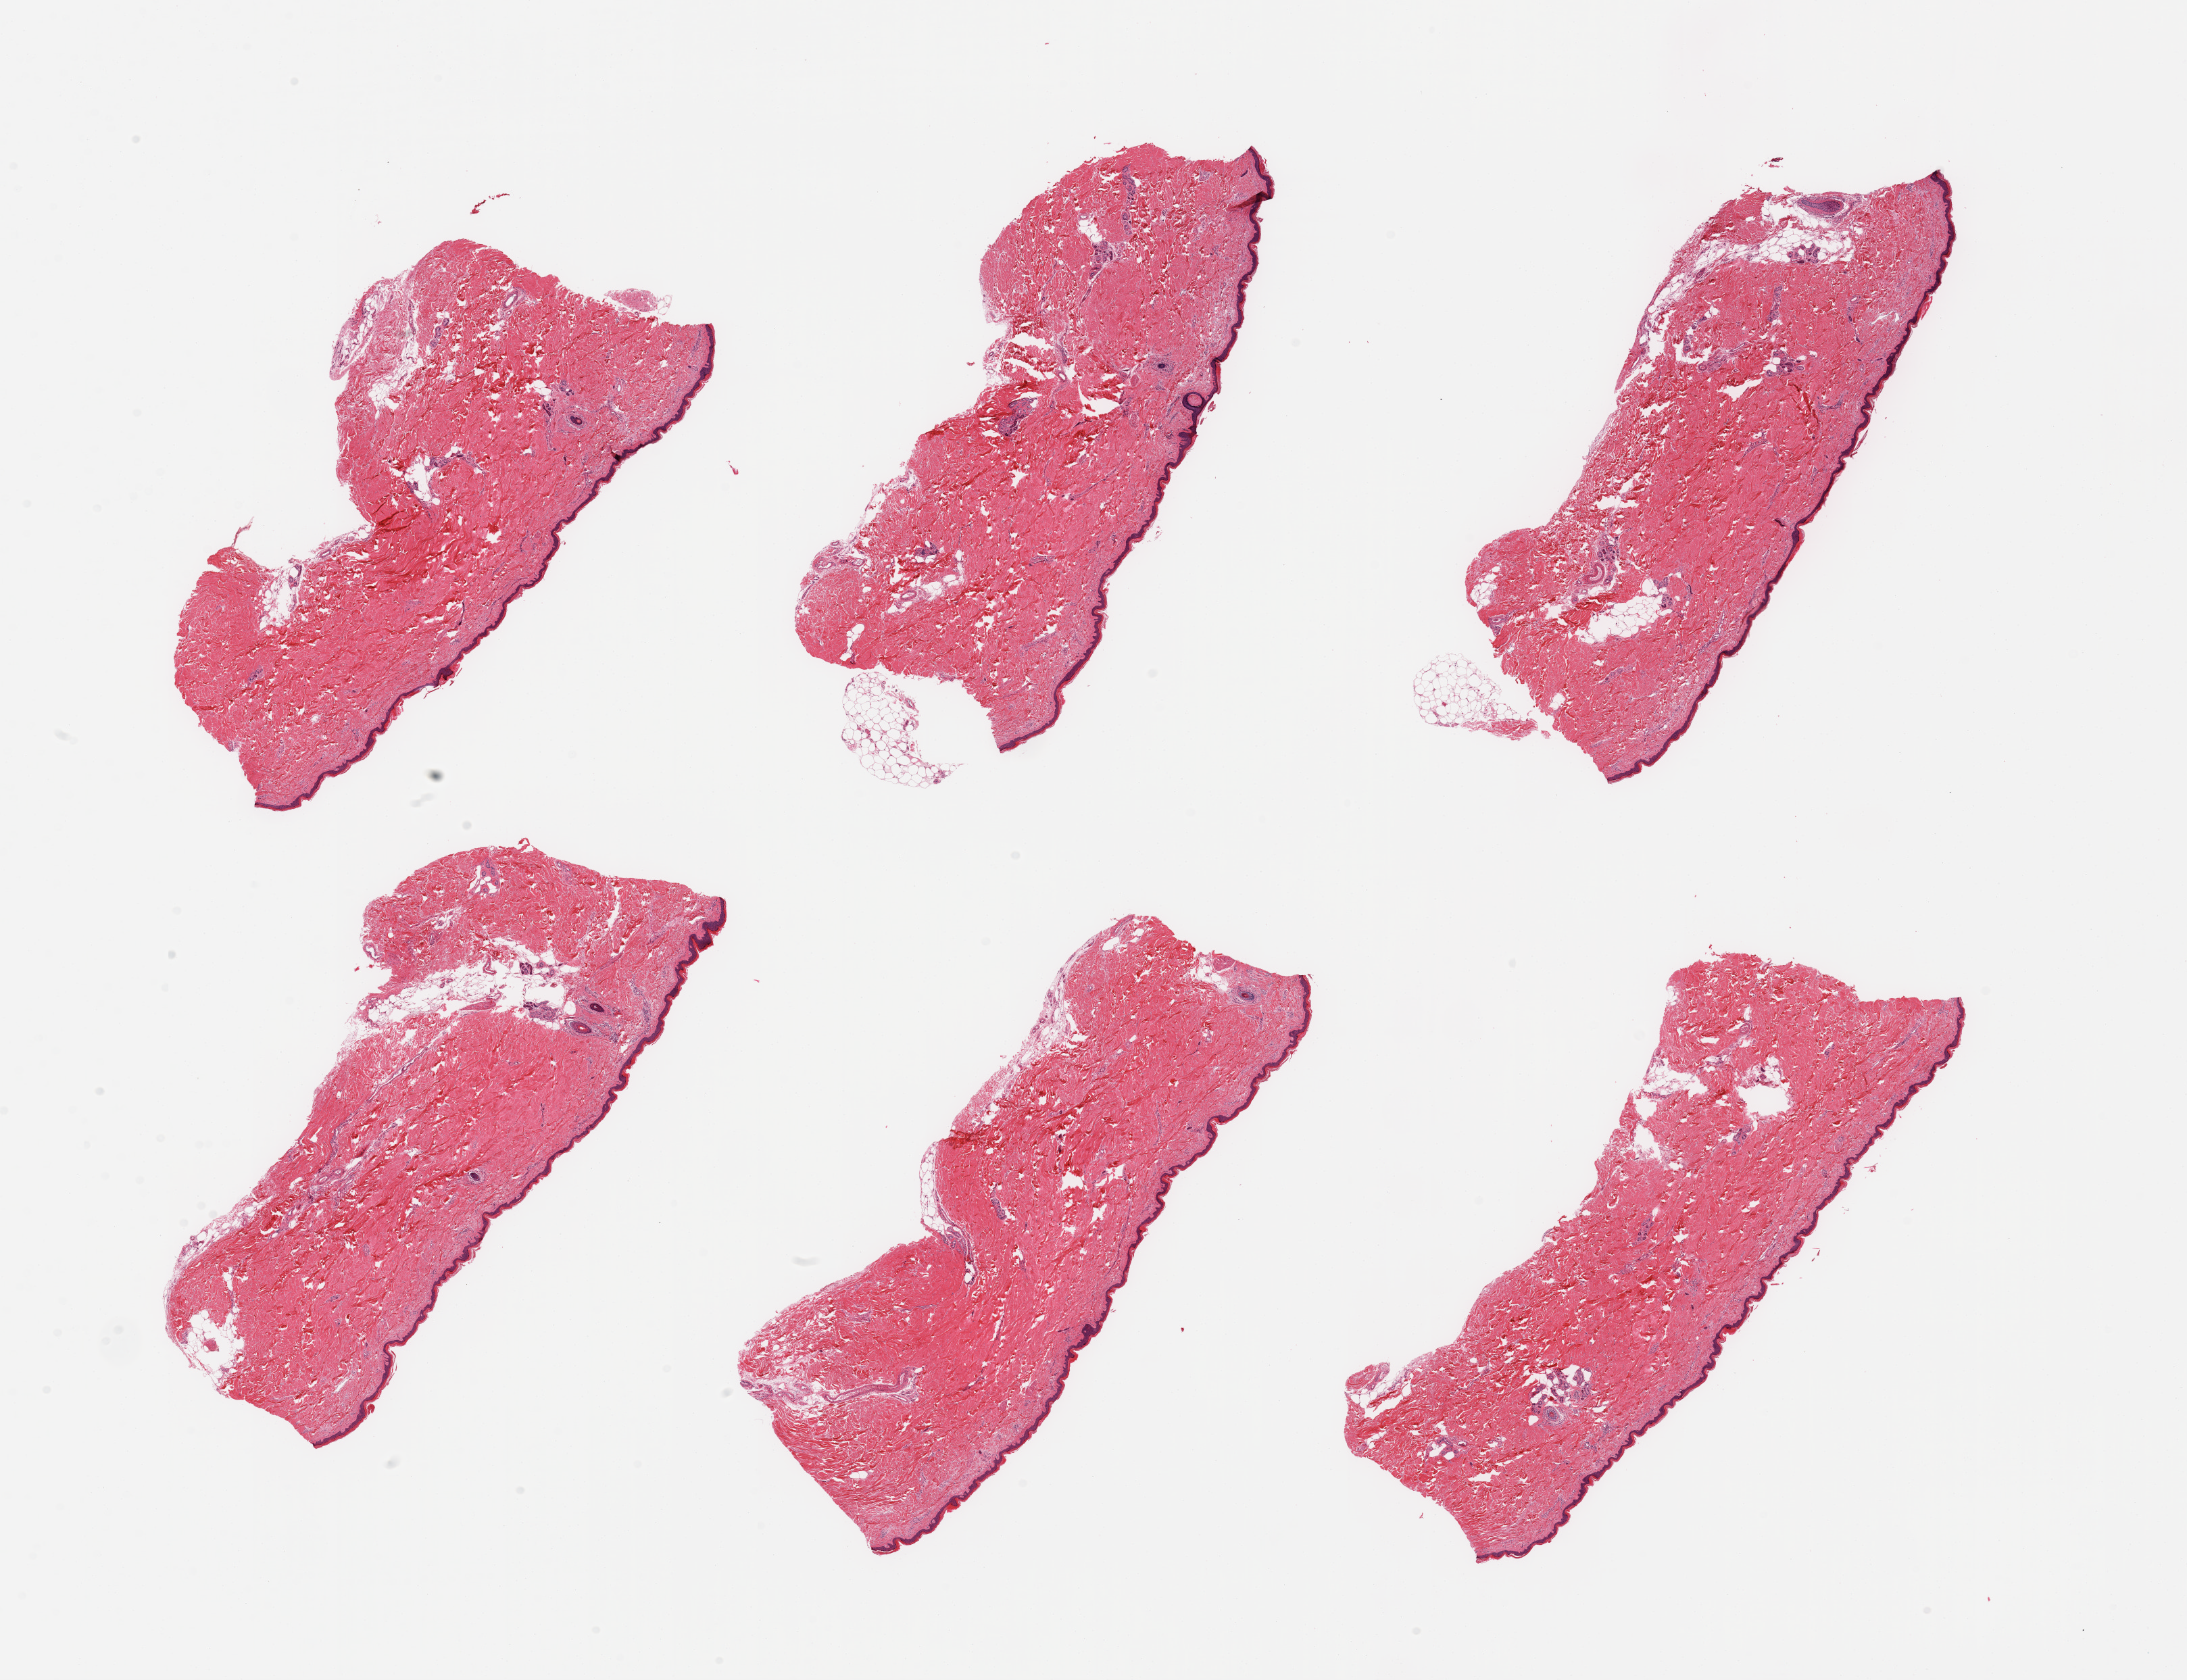
Digitized hematoxylin and eosin (H&E)-stained section, brightfield — shown as a low-resolution overview of the whole scanned area (about 25.6 x 19.7 mm, from a 20x scan). PAXgene-fixed paraffin-embedded (PFPE) section. Target tissue: skin of lower leg. Donor tissue sample. Donor: female.
- review note (as recorded): 6 pieces; well trimmed; 5% dermal fat